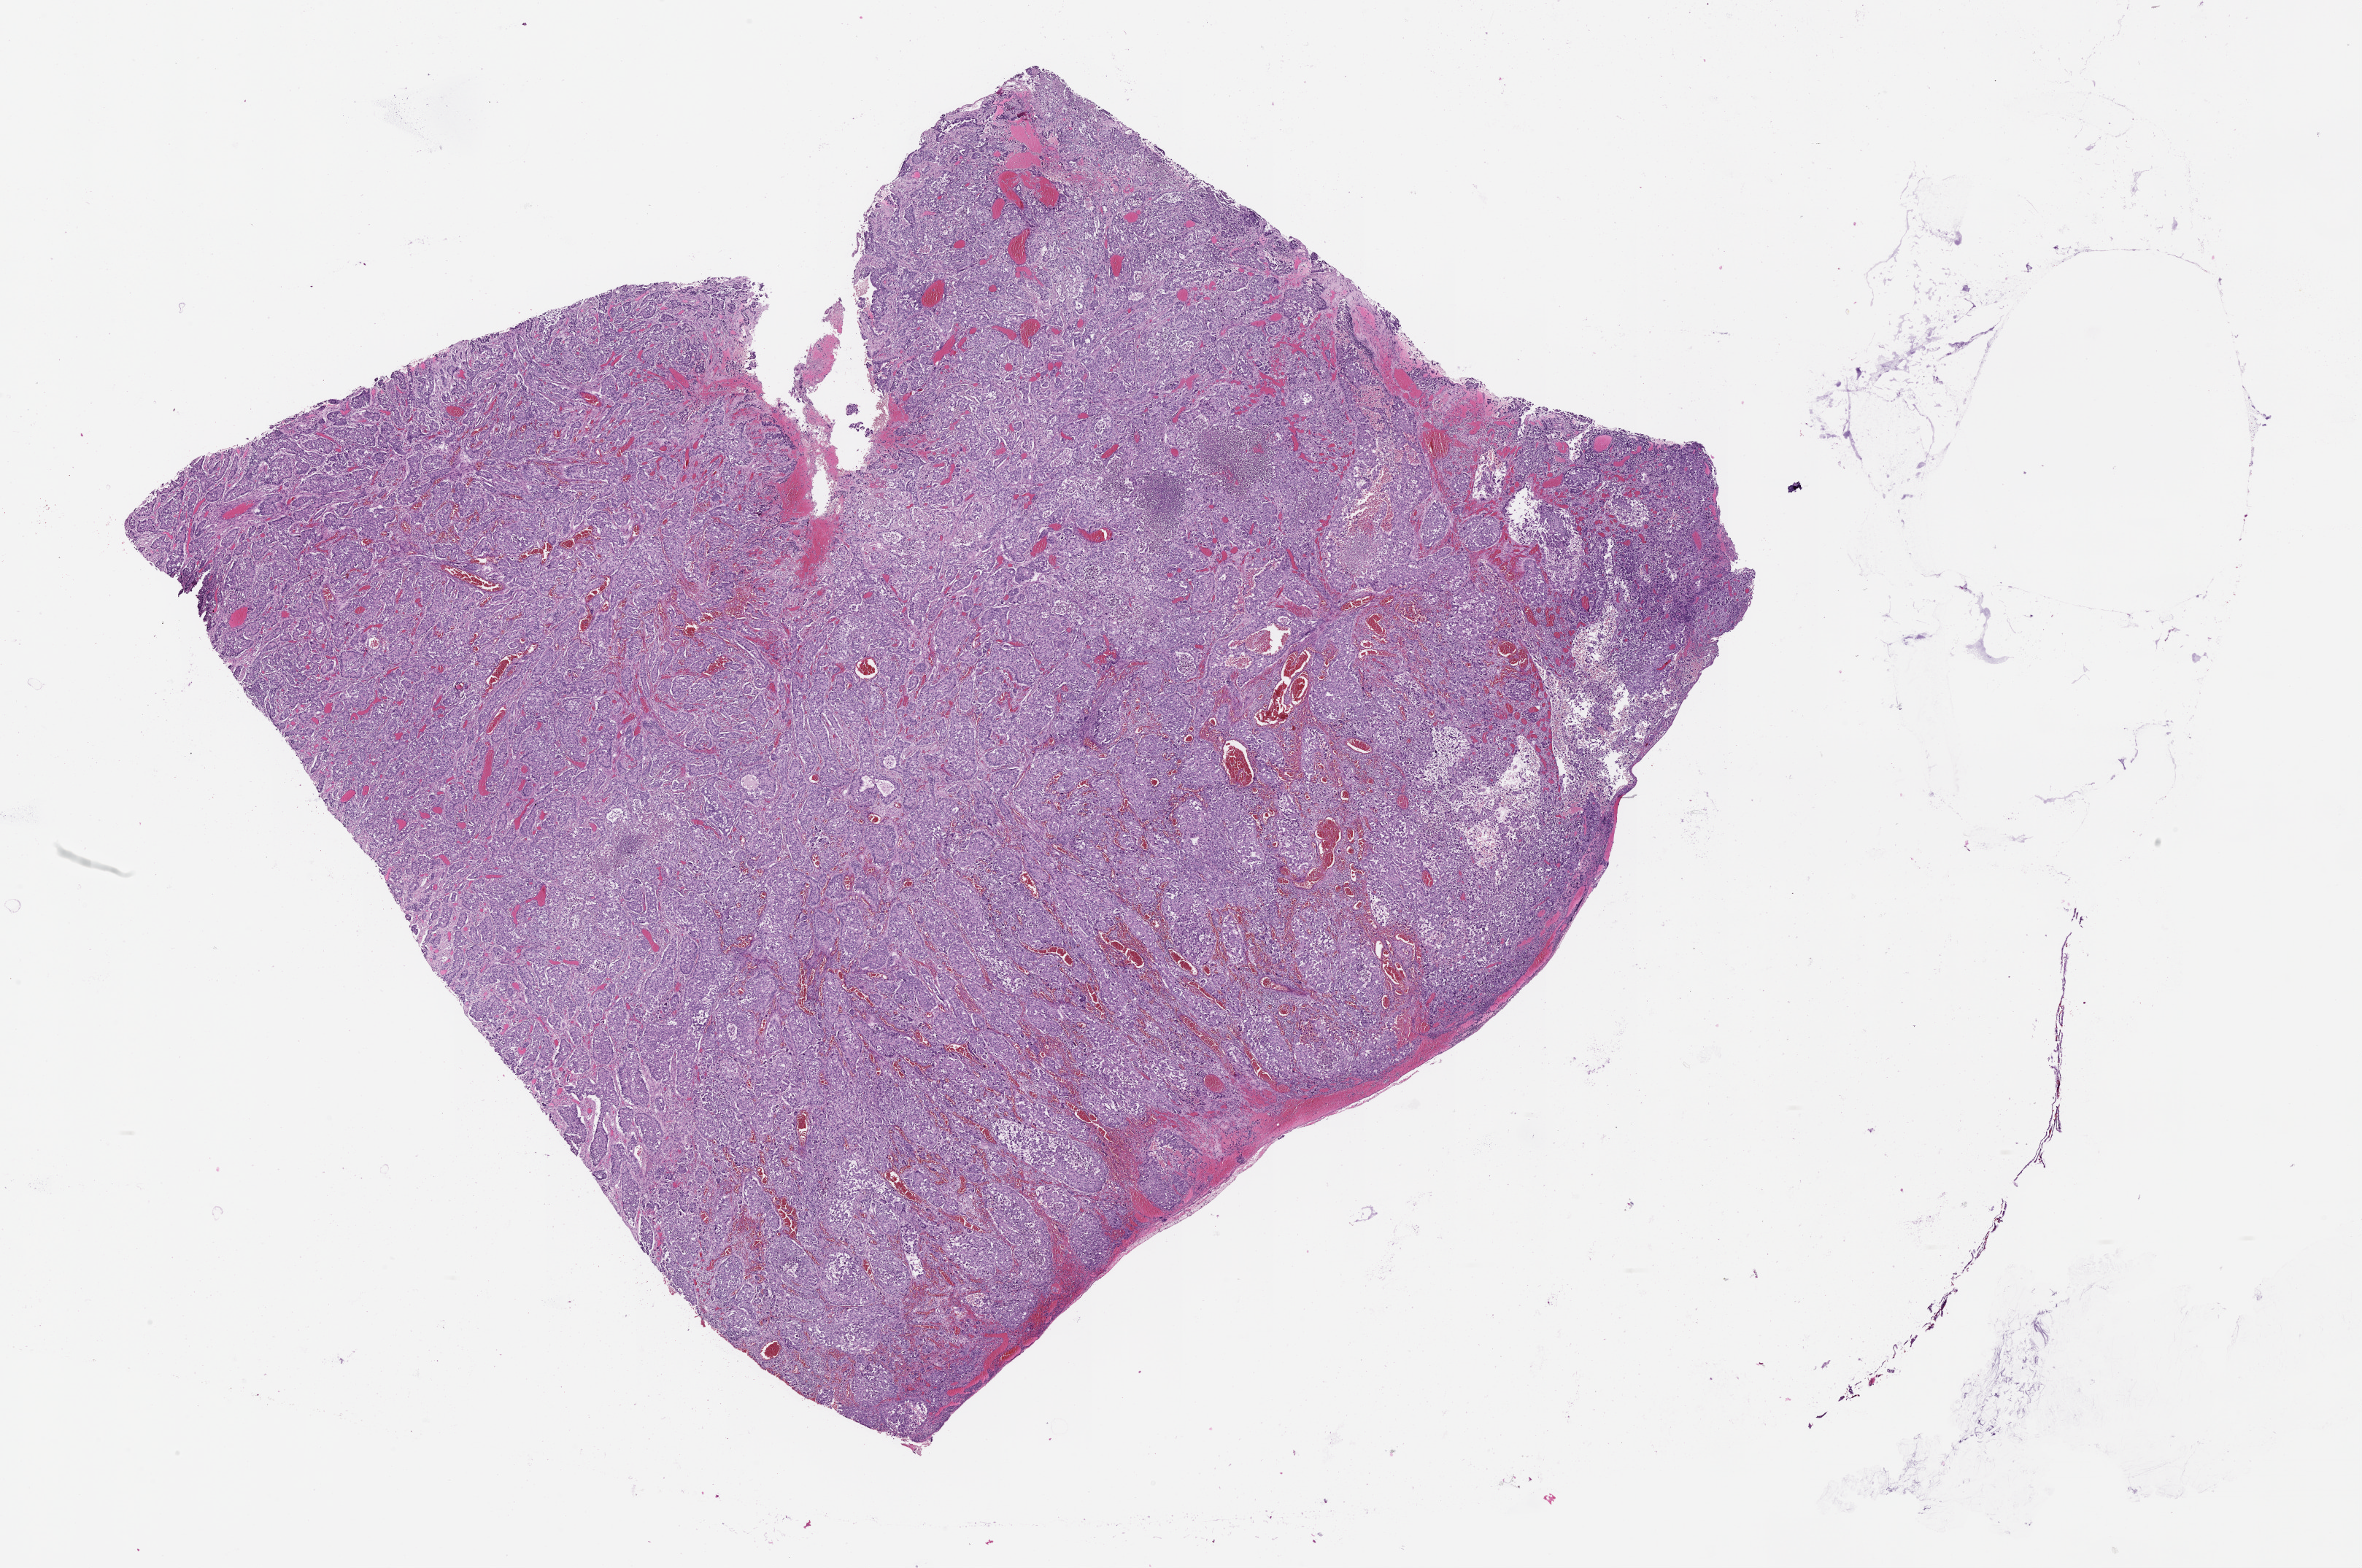
Digitized H&E-stained tissue section (whole slide) — shown as a low-resolution overview of the whole scanned area (about 26.1 x 17.3 mm). Lung, tissue type not recorded.
Patient diagnosis (cohort enrolment): squamous cell carcinoma (lung).